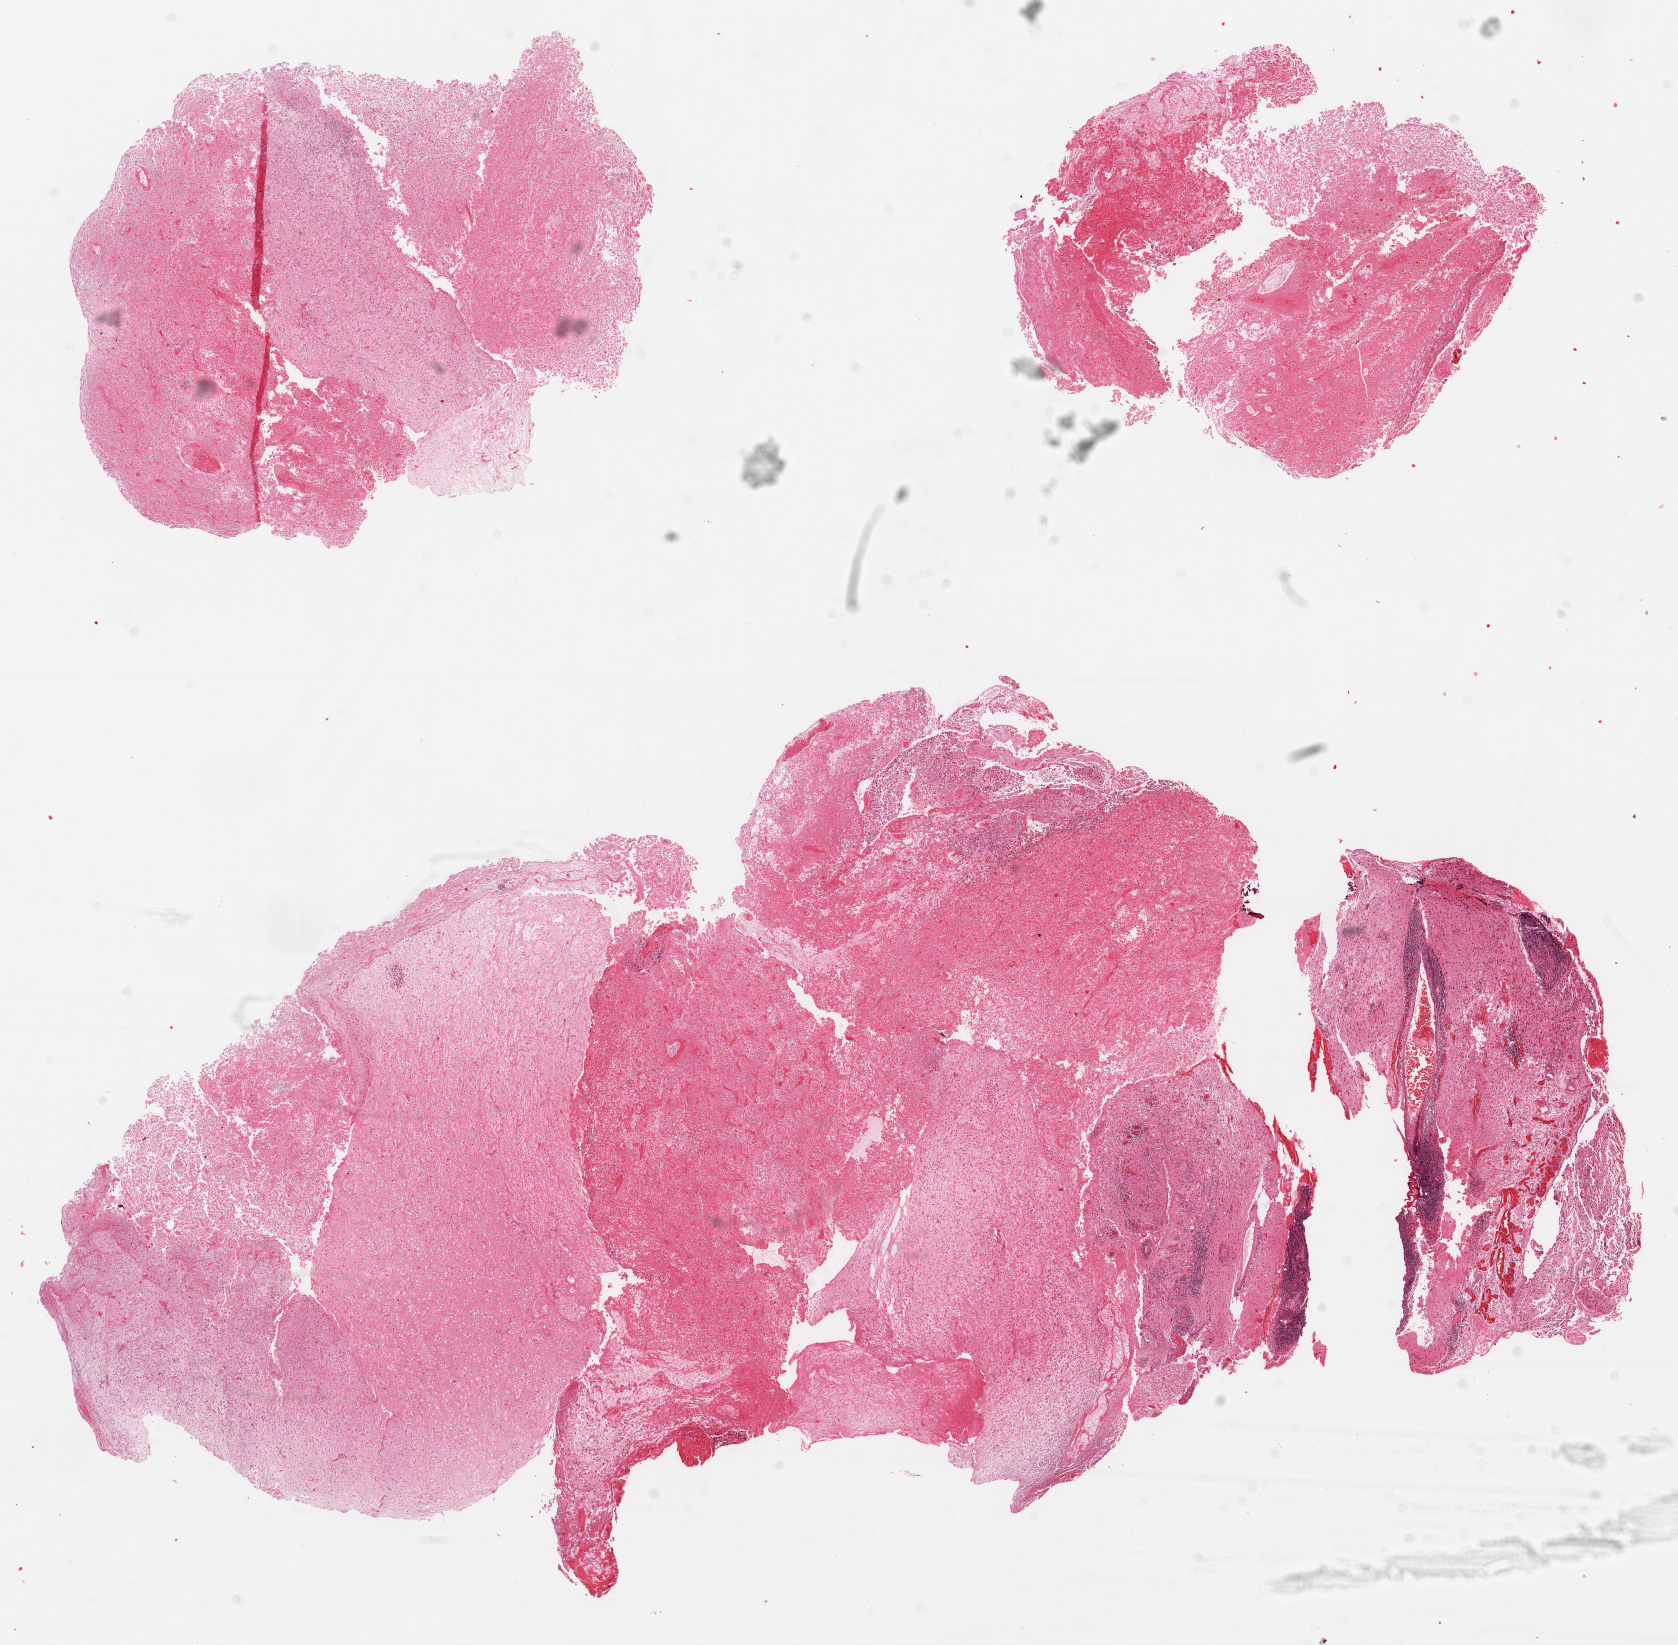
Whole-slide histology image, H&E, whole scanned area (about 13.5 x 13.3 mm) shown as a low-resolution overview, formalin-fixed paraffin-embedded (FFPE) diagnostic section, brain, primary tumour sample. Female, age 69 years at initial diagnosis.
Histologic diagnosis: Glioblastoma.